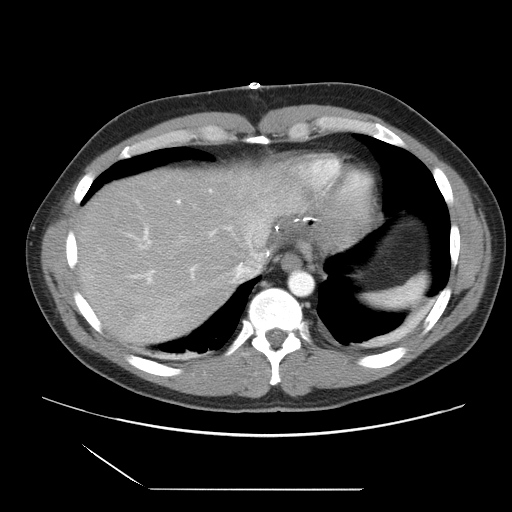
Contrast-enhanced abdominal CT, one axial slice. Position 27 of 39 along the scan axis. 120 kVp. Intravenous contrast given. Soft-tissue window (W 400 / L 40 HU). 5 mm slice thickness. 512 × 512 image matrix, field of view 395 × 395 mm. Male patient, age 39 years. Case-level facts recorded for this patient, not image findings: diagnosis: colorectal cancer liver metastases, imaged before liver resection; multiple liver metastases: yes; largest metastasis: 1.3 cm; disease in both lobes: no.
Structures marked on this image (outlined manually by an expert reader):
- hepatic veins: box from (x=163, y=253) to (x=258, y=308) px
- liver: (x=75, y=164)–(x=307, y=347)
- planned liver remnant (the part of the liver to remain after resection): (x=126, y=165)–(x=308, y=259)
- portal vein (with intrahepatic branches): (x=126, y=199)–(x=196, y=285)